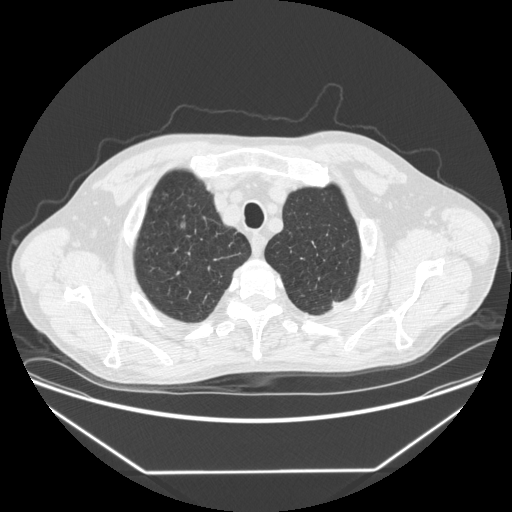
Low-dose screening chest CT, one axial slice. Position 338 of 383 along the scan axis. Reconstruction kernel STANDARD. 120 kVp. Lung window (W 1500 / L -600 HU). 512 × 512 image matrix, field of view 418 × 418 mm.
Outlined on this slice (expert manual segmentation):
- lesion 1 (tumor, upper lobe of left lung): bounding box [x1, y1, x2, y2] px = [331, 301, 337, 306]